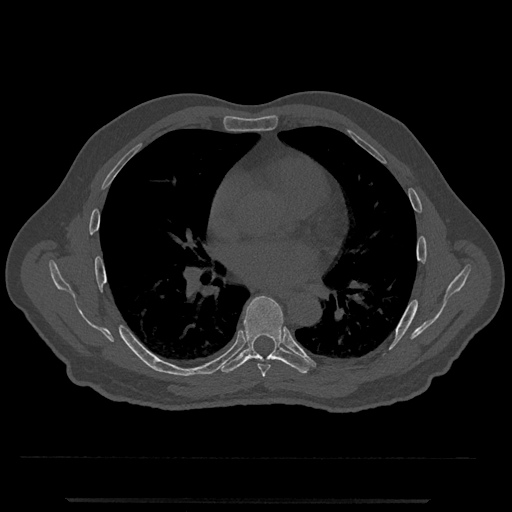
CT including the spine, one axial slice; position 704 of 797 along the scan axis; reconstruction kernel Br40s/3; 120 kVp; bone window (W 1800 / L 400 HU); 512 × 512 image matrix, field of view 419 × 419 mm. Male patient, age 63 years. Case-level facts recorded for this patient, not image findings: primary cancer: prostate.
Annotated regions visible in this slice (semi-automatic segmentation, software-assisted and operator-edited):
- T6 vertebra: bounding box [x1, y1, x2, y2] px = [258, 364, 271, 377]
- T7 vertebra: [219, 295, 311, 374]